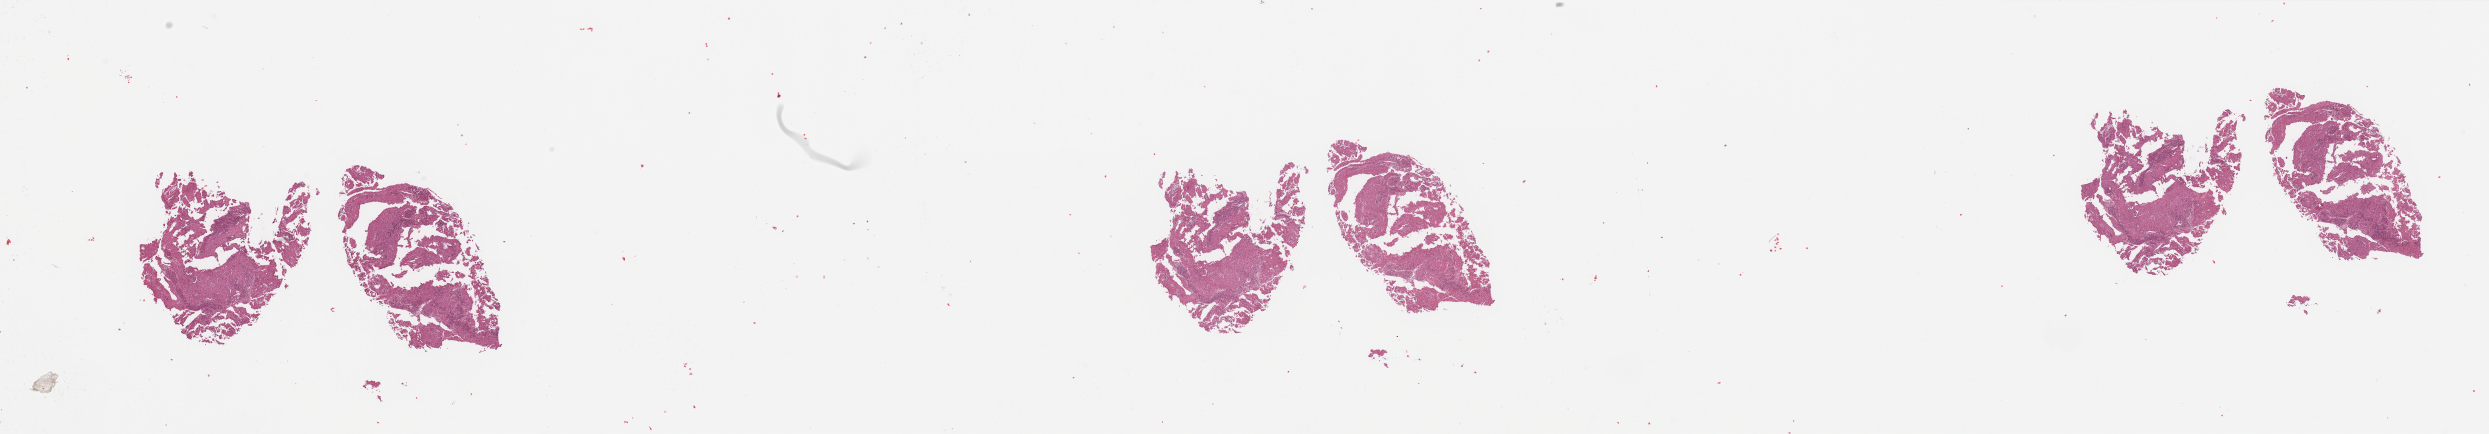
Digitized H&E tissue section (whole slide) — whole scanned area (about 39.4 x 6.9 mm) shown as a low-resolution overview. Tumour tissue sample, sampled site: lung. Female, 60 y/o. Composition of this section per pathologist review: tumour nuclei 85%, necrosis 0%.
Histologic diagnosis: Adenocarcinoma, NOS.